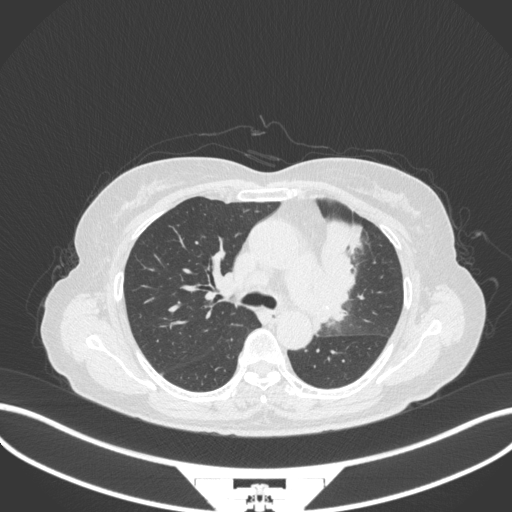
Chest CT, one axial slice. Position 219 of 382 along the scan axis. Reconstruction kernel B31f. Lung window (W 1500 / L -600 HU). 512 × 512 image matrix, field of view 400 × 400 mm. Patient: female, 64 years. From the clinical record (not read from this slice): clinical TNM (as recorded): T2a N2 M0.
Annotated regions visible in this slice (rectangle marked by the reading radiologist):
- lung tumour (recorded histology: adenocarcinoma): bounding box <323,216,366,321> (left, top, right, bottom; pixels)